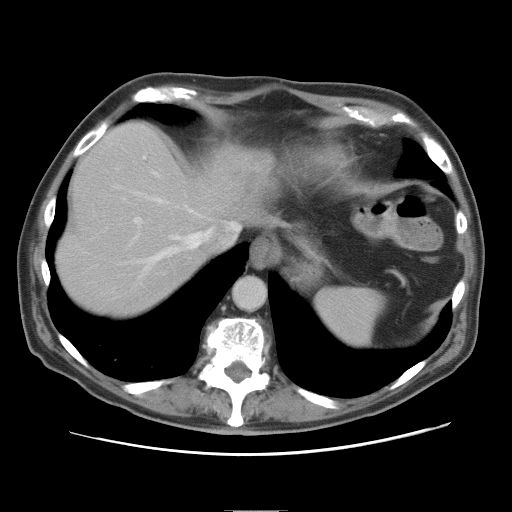
Contrast-enhanced abdominal CT, one axial slice. Position 67 of 89 along the scan axis. Intravenous contrast given. Soft-tissue window (W 400 / L 40 HU). 5 mm slice thickness. 512 × 512 image matrix, field of view 375 × 375 mm. Male patient, age 69 years. Case-level facts recorded for this patient, not image findings: diagnosis: colorectal cancer liver metastases, imaged before liver resection; multiple liver metastases: no; largest metastasis: 8.5 cm; disease in both lobes: no.
Annotated regions visible in this slice (manually delineated by an expert):
- hepatic veins: box from (x=116, y=169) to (x=240, y=279) px
- liver: (x=57, y=123)–(x=254, y=317)
- planned liver remnant (the part of the liver to remain after resection): (x=57, y=123)–(x=238, y=317)
- portal vein (with intrahepatic branches): (x=133, y=156)–(x=145, y=239)